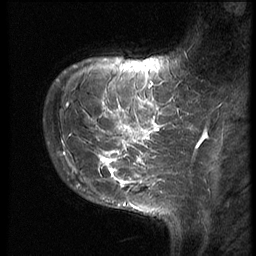
Breast MRI (dynamic contrast-enhanced), one sagittal slice; position 11 of 62 along the scan axis; 3 images stored at this slice position (order not interpretable as contrast timing); 1.5 T; TE 4.2 ms, TR 9 ms; 2.5 mm slice thickness; 256 × 256 image matrix, field of view 180 × 180 mm. Female patient, age 28 years. From the clinical record (not read from this slice): setting: breast cancer imaged before/during neoadjuvant chemotherapy.
Outlined on this slice (semi-automatically segmented with operator editing):
- analysis volume of interest (the breast-tissue region the enhancement analysis was run in; not a lesion): bounding box <44,78,192,190> (left, top, right, bottom; pixels)
- tumour enhancement mask (voxels above the 140 % enhancement threshold inside the analysis volume of interest): <62,100,192,187>